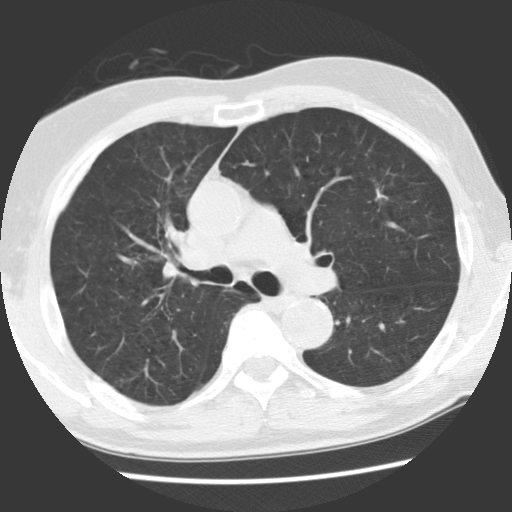
Low-dose screening chest CT, axial slice. Baseline annual screen. Lung window (W 1500 / L -600 HU). Standard (soft-tissue) reconstruction kernel (STANDARD). 140 kVp. Slice 81 of 131 in the series. Male participant, aged 70 years at enrolment. Current smoker at enrolment.
- Lesion marked by an expert reader, bounding box (x1, y1, x2, y2) in pixels: (349, 177, 401, 223).
- The screening reader recorded 2 non-calcified nodules or masses ≥4 mm on this exam (left upper lobe, right lower lobe); which of them this box marks is not recorded.
- Lung cancer was diagnosed 879 days after this screen (after the third annual screen): adenocarcinoma, NOS, left upper lobe, moderately differentiated (G2), stage IIIA (AJCC 6th edition), 17 mm at pathology.